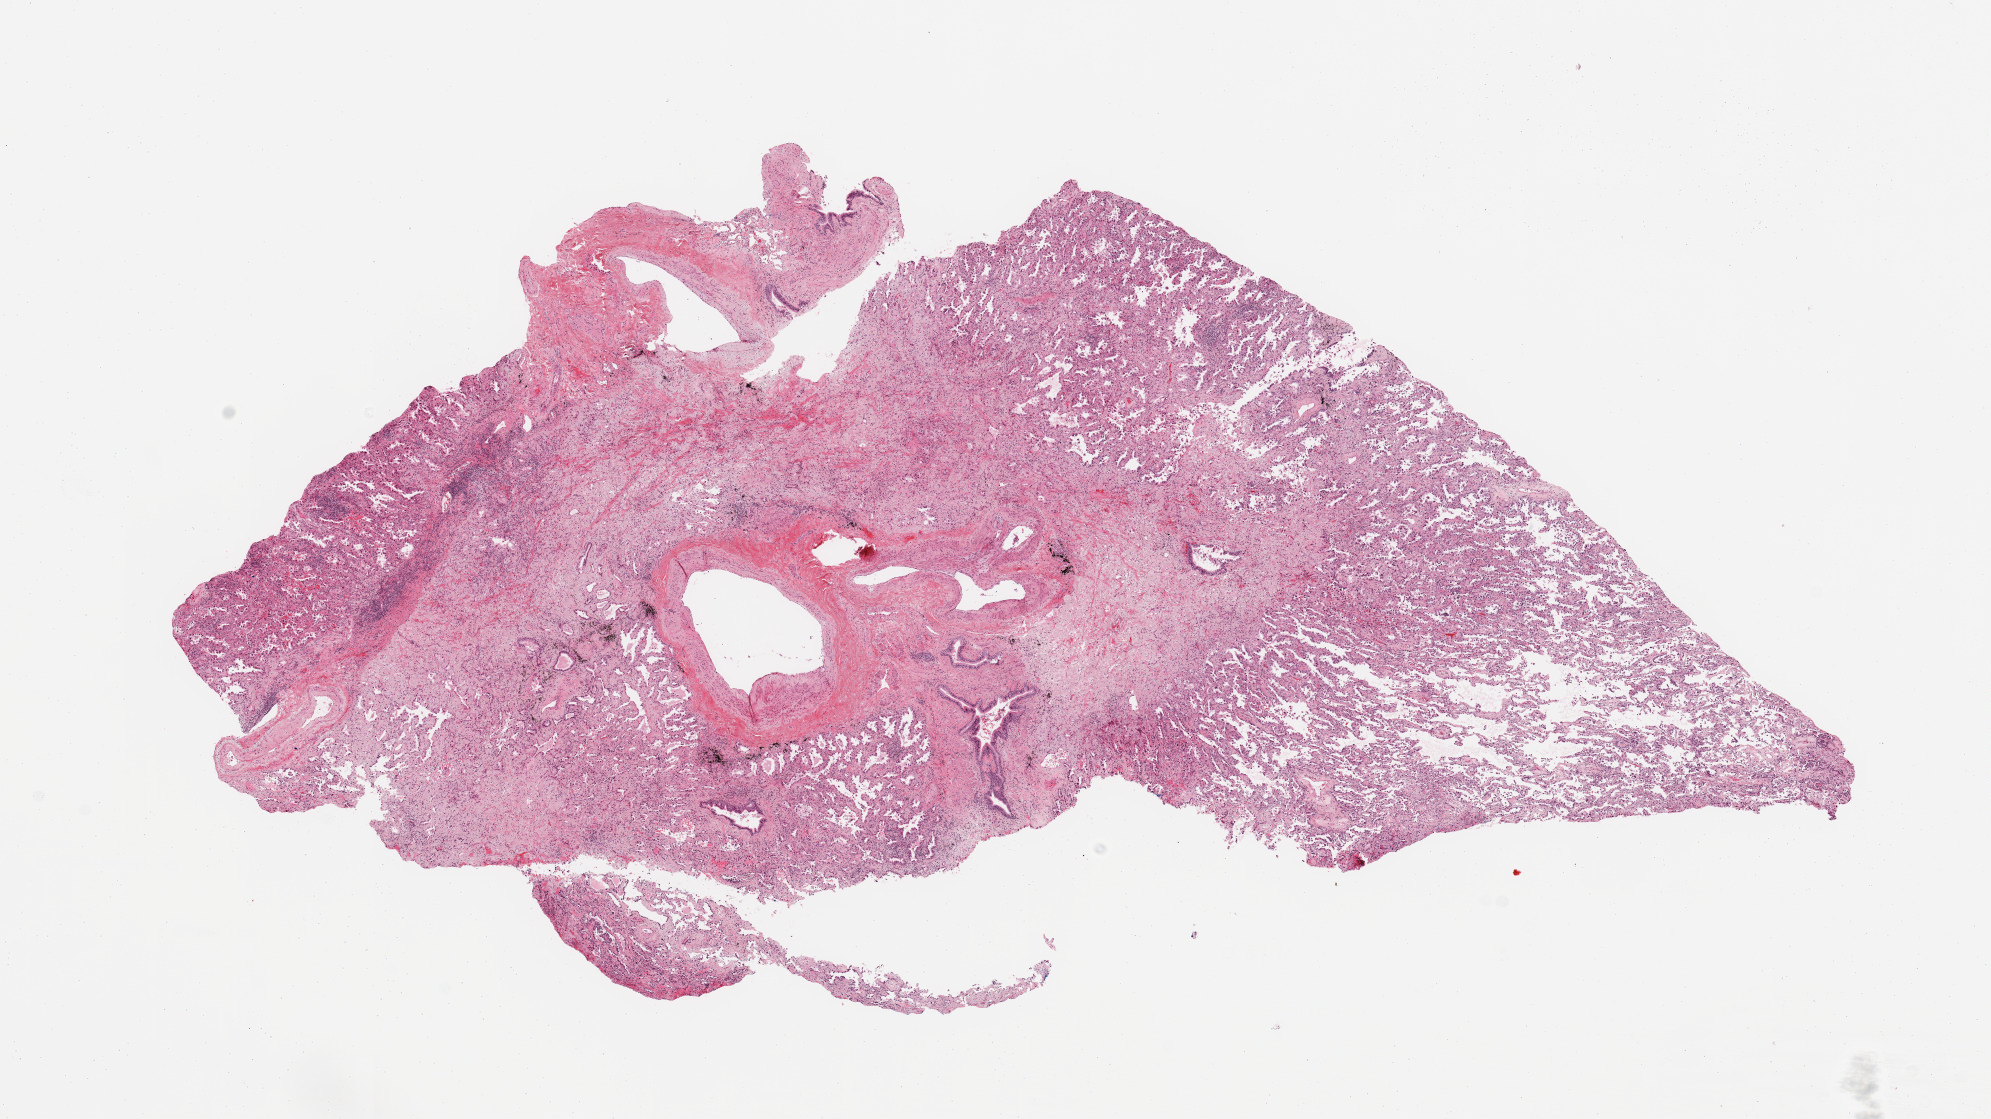
H&E whole-slide image — shown as a low-resolution overview of the whole scanned area (about 15.8 x 8.9 mm). Tumour tissue sample, sampled site: lung. Patient: male, age 74 years.
Diagnosis: Adenocarcinoma, NOS.